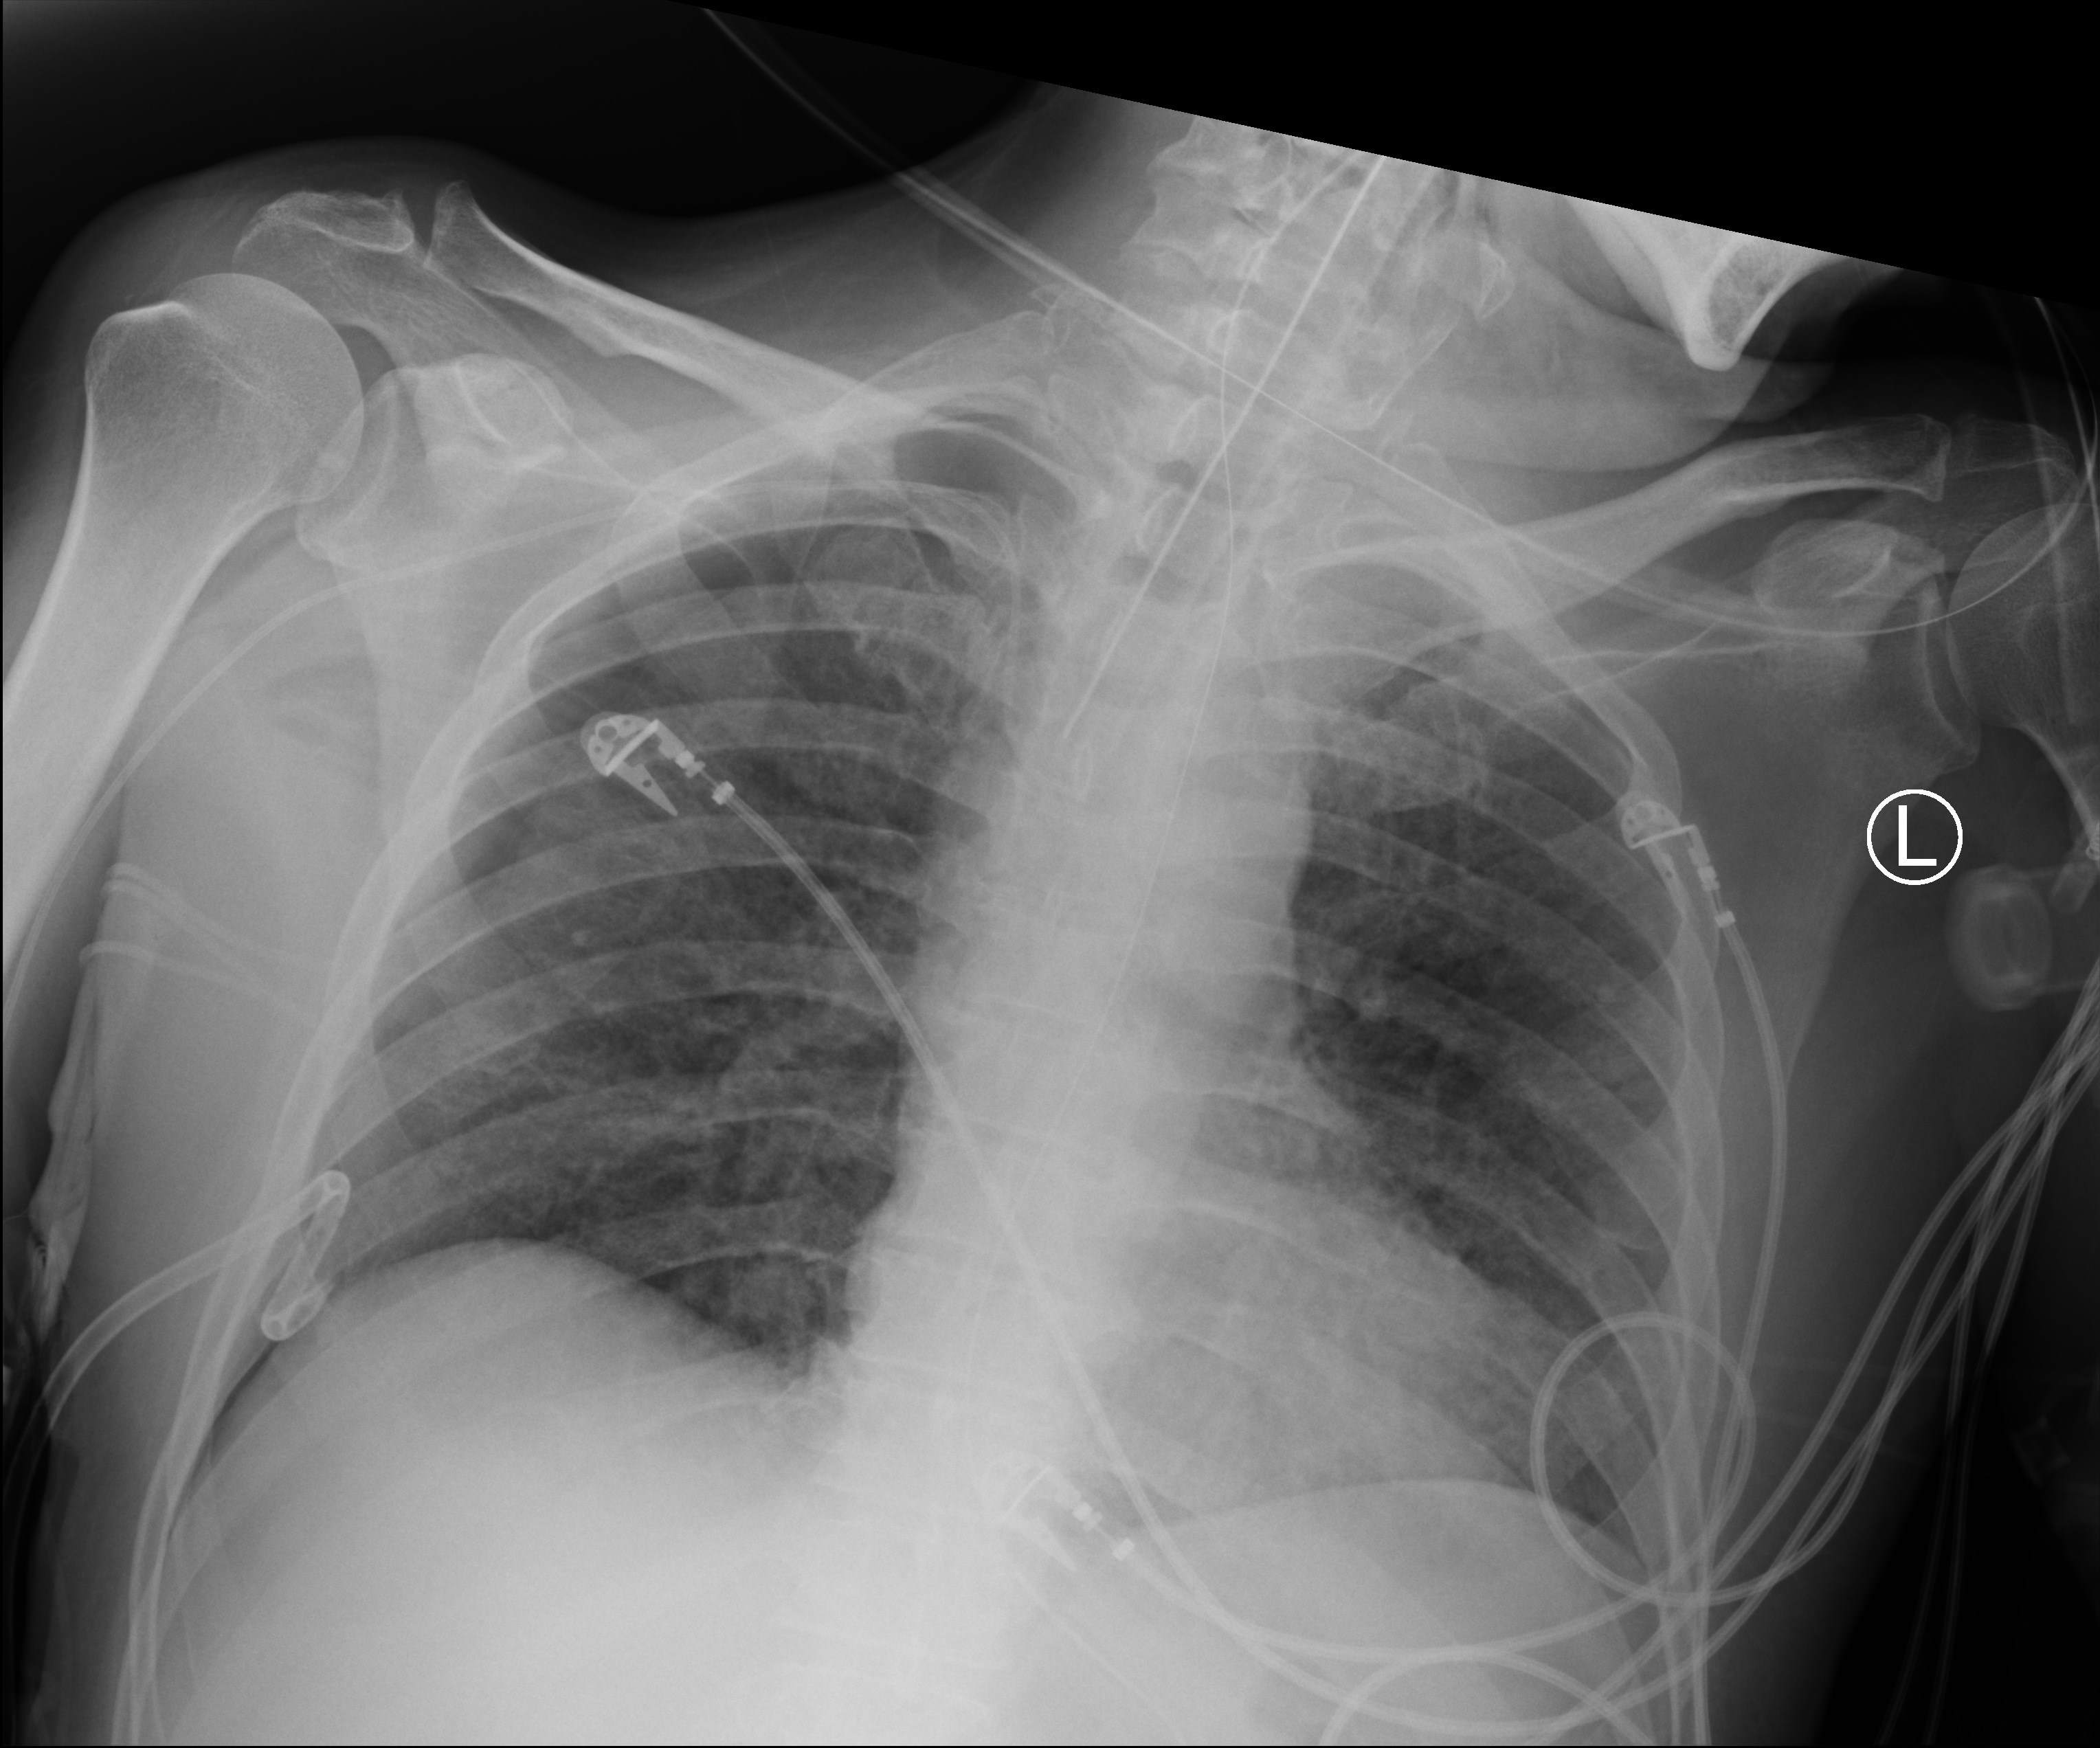
Chest X-ray (portable), anteroposterior (AP) projection. Patient hospitalised with COVID-19; male, aged 18–59 years.
Hospital-stay facts (about this admission, not read from this image; timing relative to this image not recorded): admitted to intensive care during this hospital stay: yes; mechanically ventilated during this hospital stay: yes; other chronic lung disease (admission record): no.